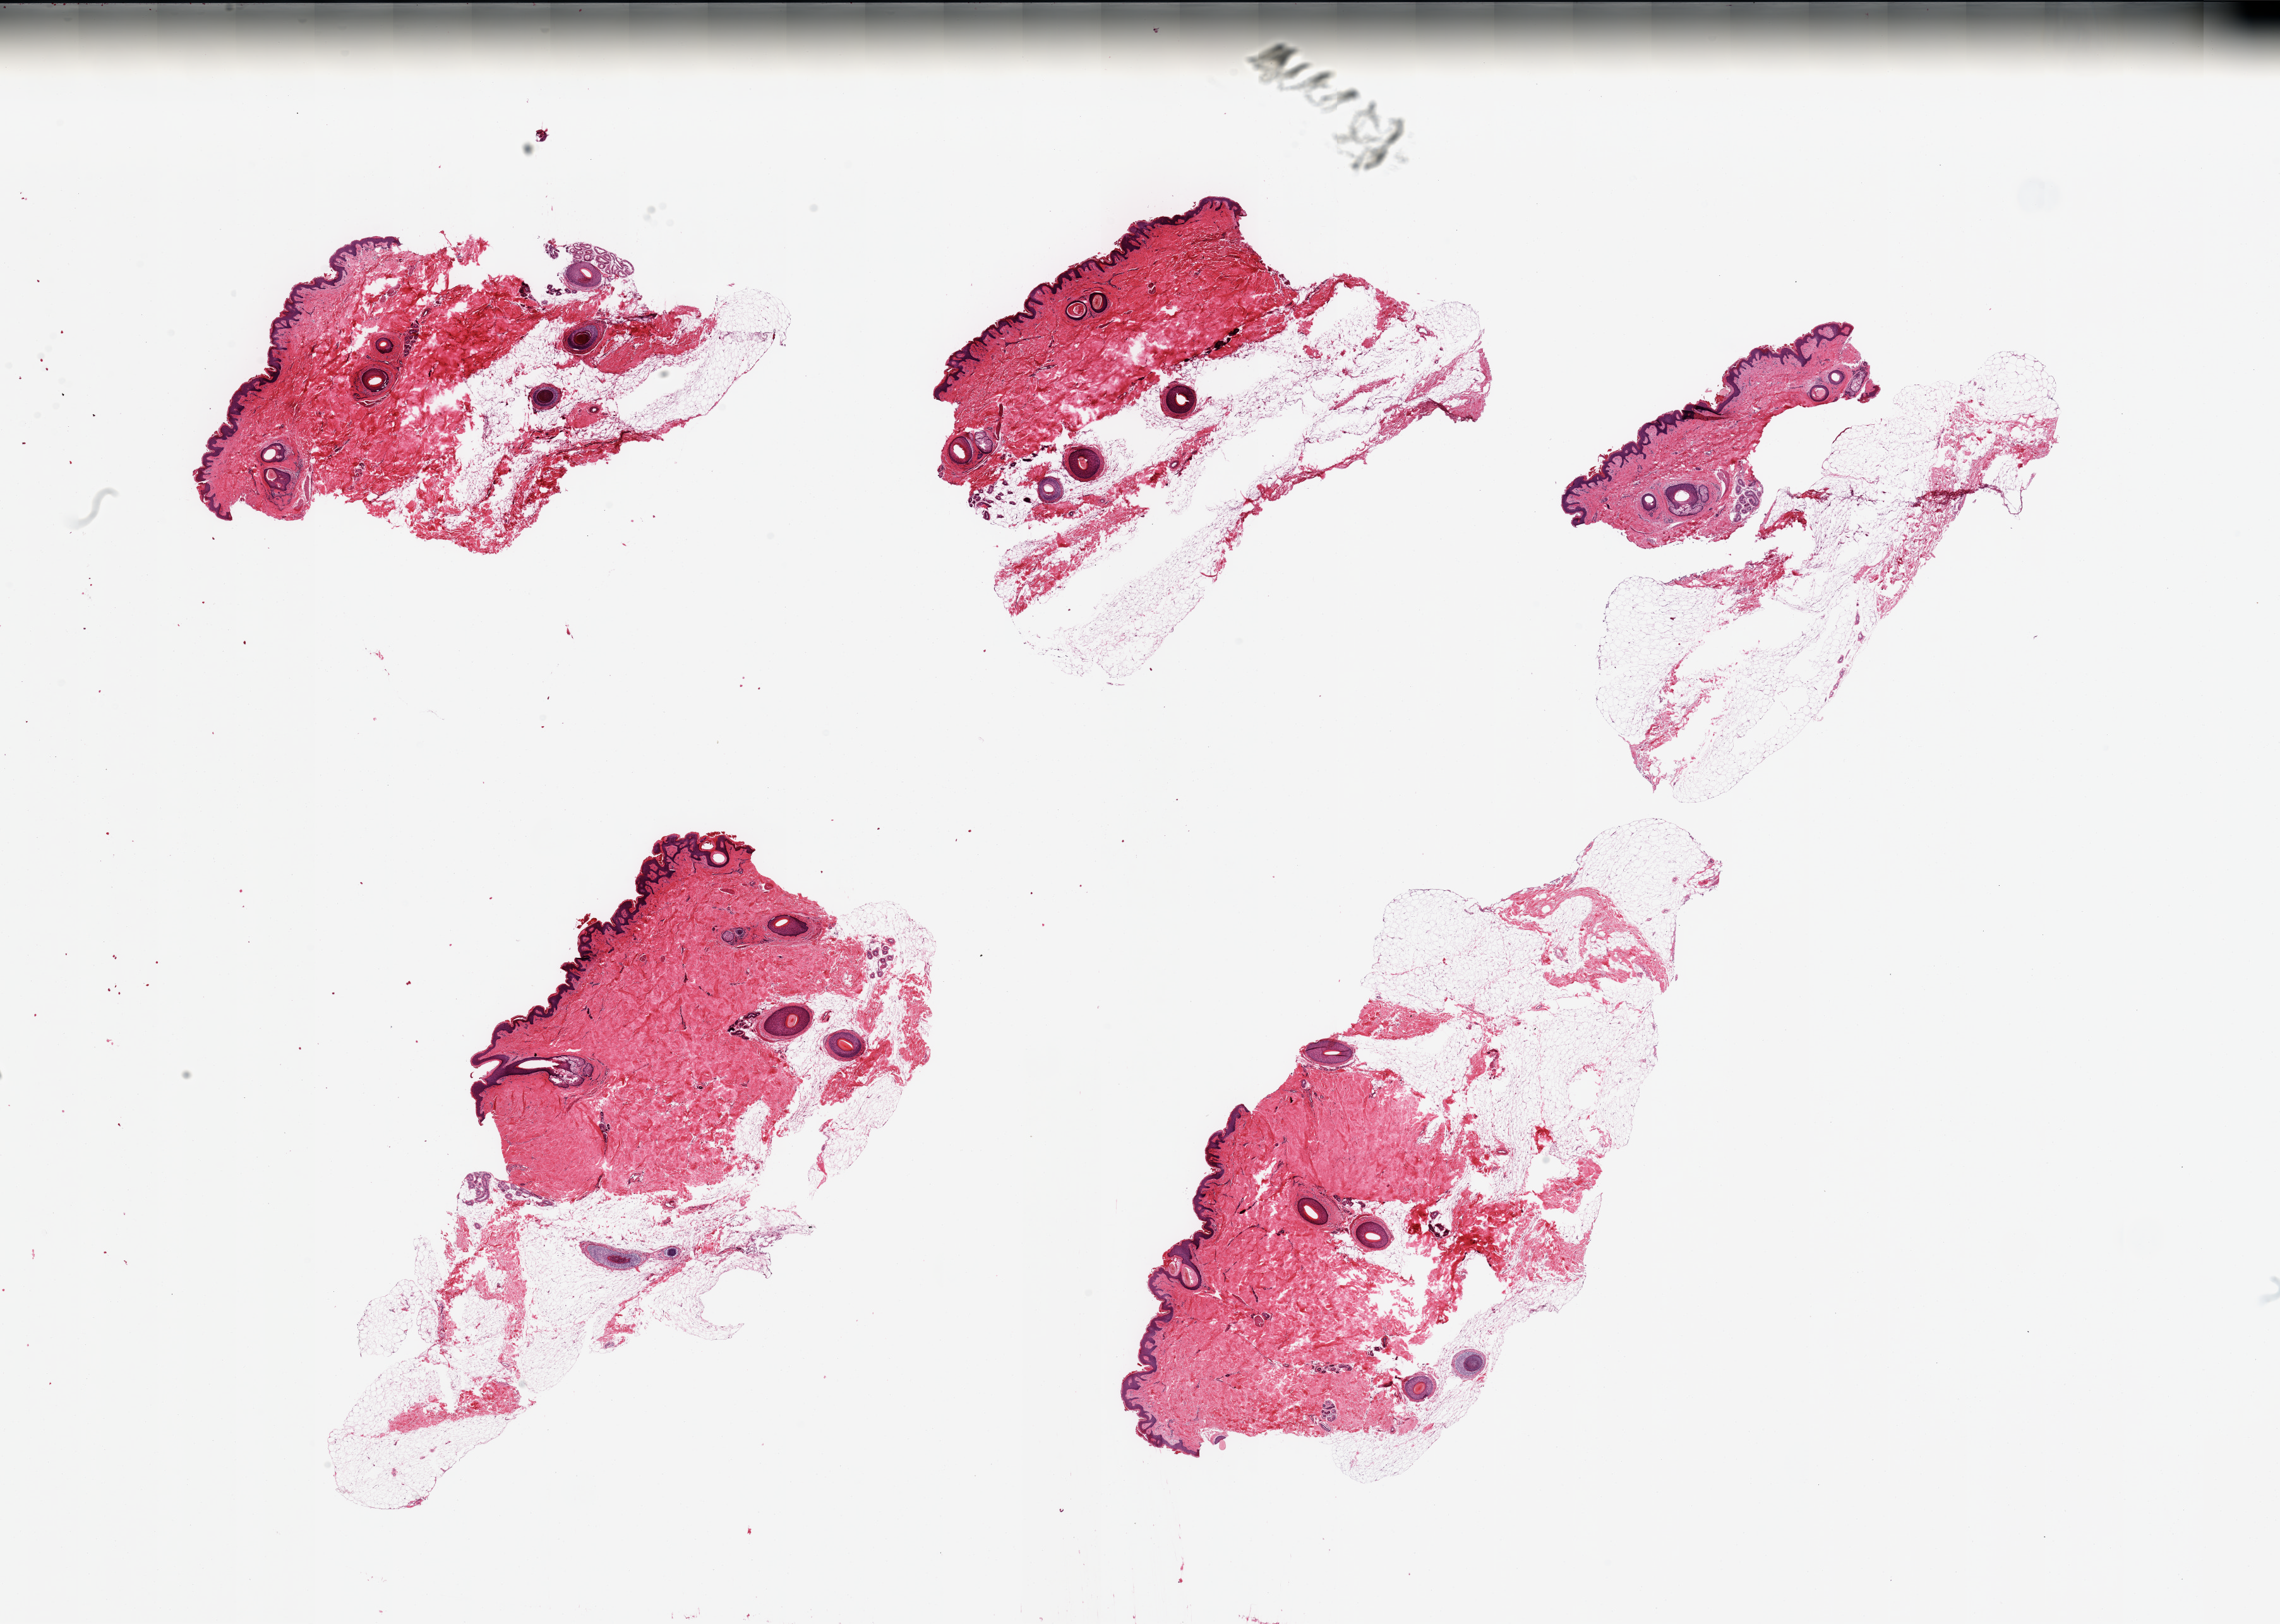
Digitized hematoxylin and eosin (H&E)-stained section, whole scanned area (about 28.5 x 20.3 mm) shown as a low-resolution overview, PAXgene-fixed, paraffin-embedded tissue, target tissue: skin of suprapubic region, tissue donor sample. Donor sex: male.
* review note (as recorded): 5 pieces; abundant untrimmed subcutaneous fat; up to 7 hairs per piece